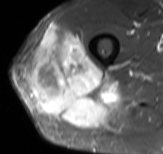
MRI of an extremity soft-tissue mass, one axial slice; position 46 of 61 along the scan axis; STIR; MR volume resampled by the dataset authors to the PET/CT grid (not the native acquisition matrix); 3.27 mm slice thickness; 163 × 154 image matrix, field of view 159 × 150 mm. Male patient. From the clinical record (not read from this slice): histological type: poorly differentiated synovial sarcoma; grade: high; site of the primary tumour: right buttock.
Structures marked on this image (expert contour drawn on MRI and transferred to this co-registered scan by the dataset authors):
- gross tumour volume including surrounding oedema: bounding box <29,25,117,127> (left, top, right, bottom; pixels)
- gross tumour volume (mass): <29,25,113,127>